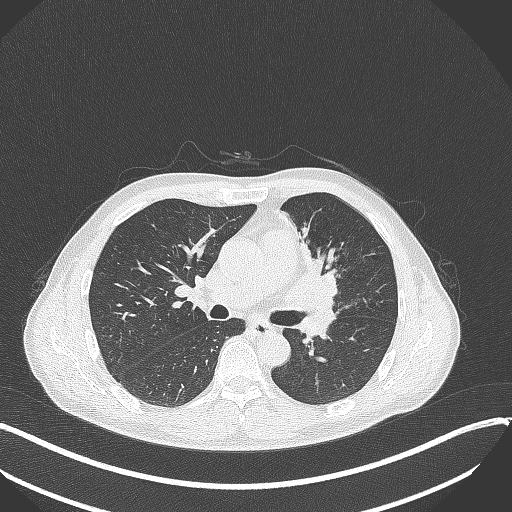
Chest CT, one axial slice; slice 194 of 411 in the series (ordered by position); reconstruction kernel B70f; 120 kVp; lung window (W 1500 / L -600 HU); 512 × 512 image matrix, field of view 400 × 400 mm. Male patient, age 56 years. From the clinical record (not read from this slice): clinical TNM (as recorded): T2a N0 M0.
Outlined on this slice (bounding box drawn by a radiologist):
- lung tumour (recorded histology: squamous cell carcinoma): bounding box <280,257,340,314> (left, top, right, bottom; pixels)